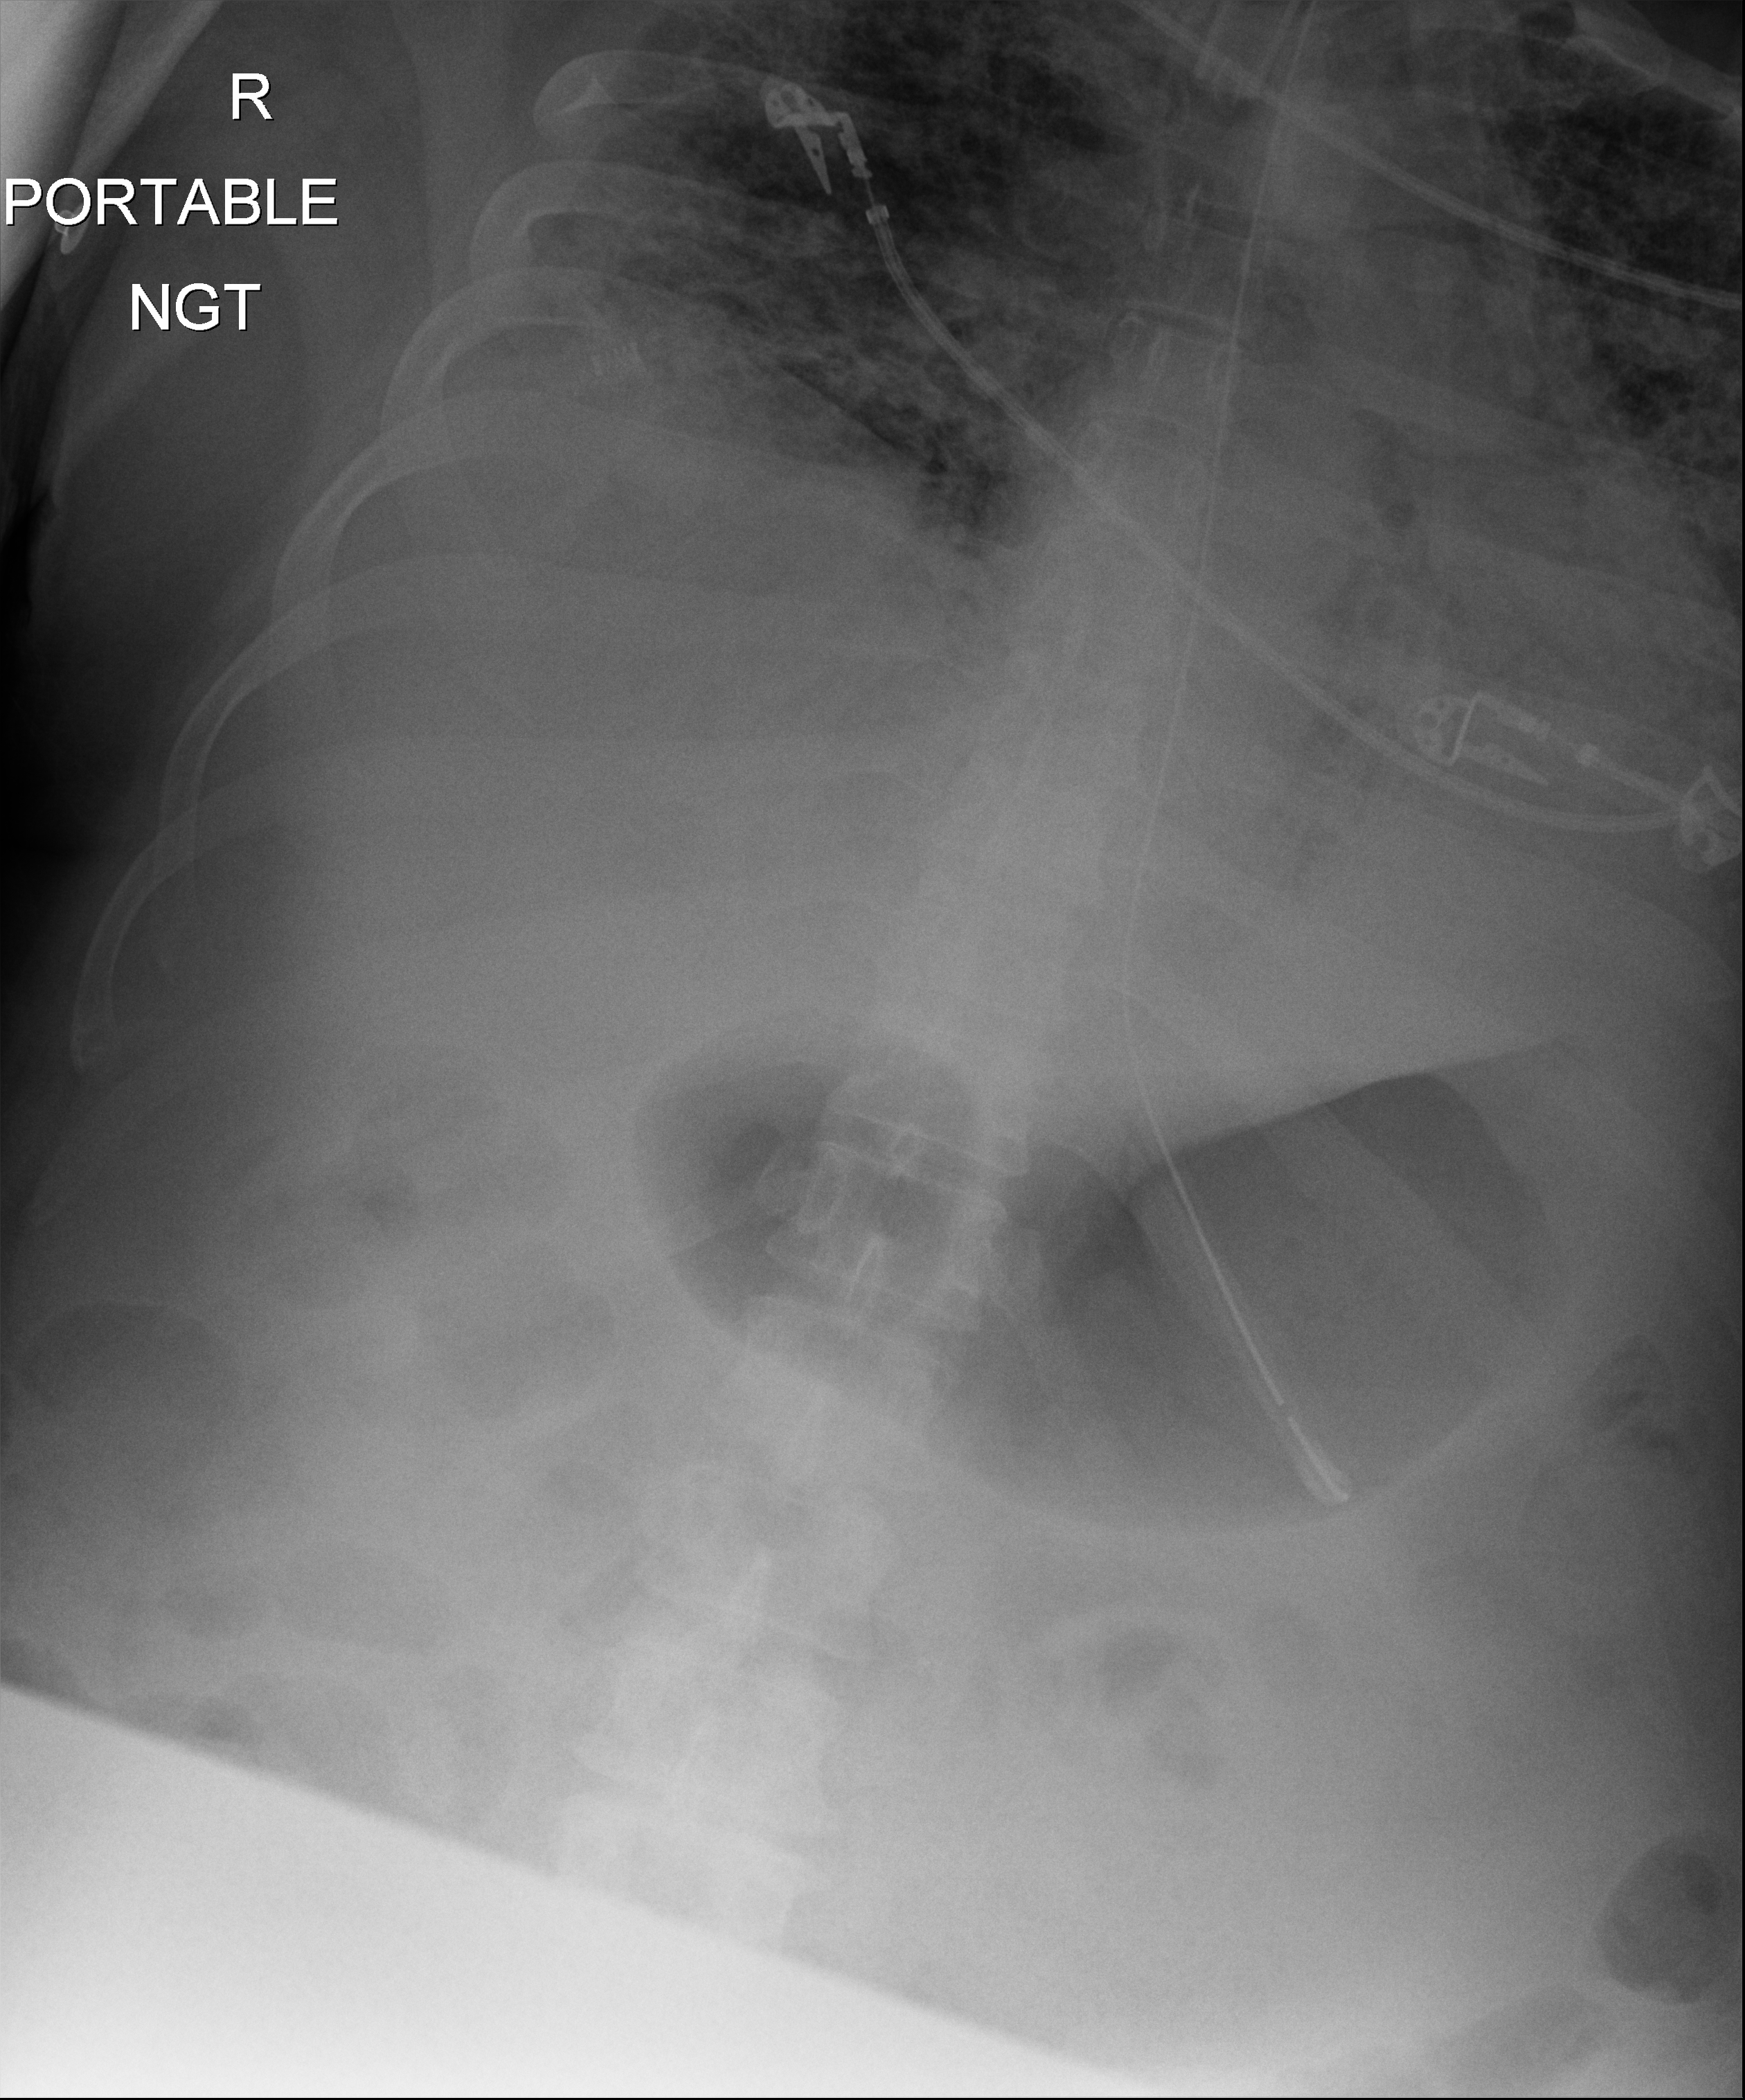
Chest X-ray (portable), anteroposterior (AP) projection. Male patient hospitalised with COVID-19, age 18–59 years.
Admission-level facts for this patient (not findings on this image; timing relative to this image not recorded):
- length of hospital stay: 96 days
- admitted to intensive care during this hospital stay: yes
- mechanically ventilated during this hospital stay: yes